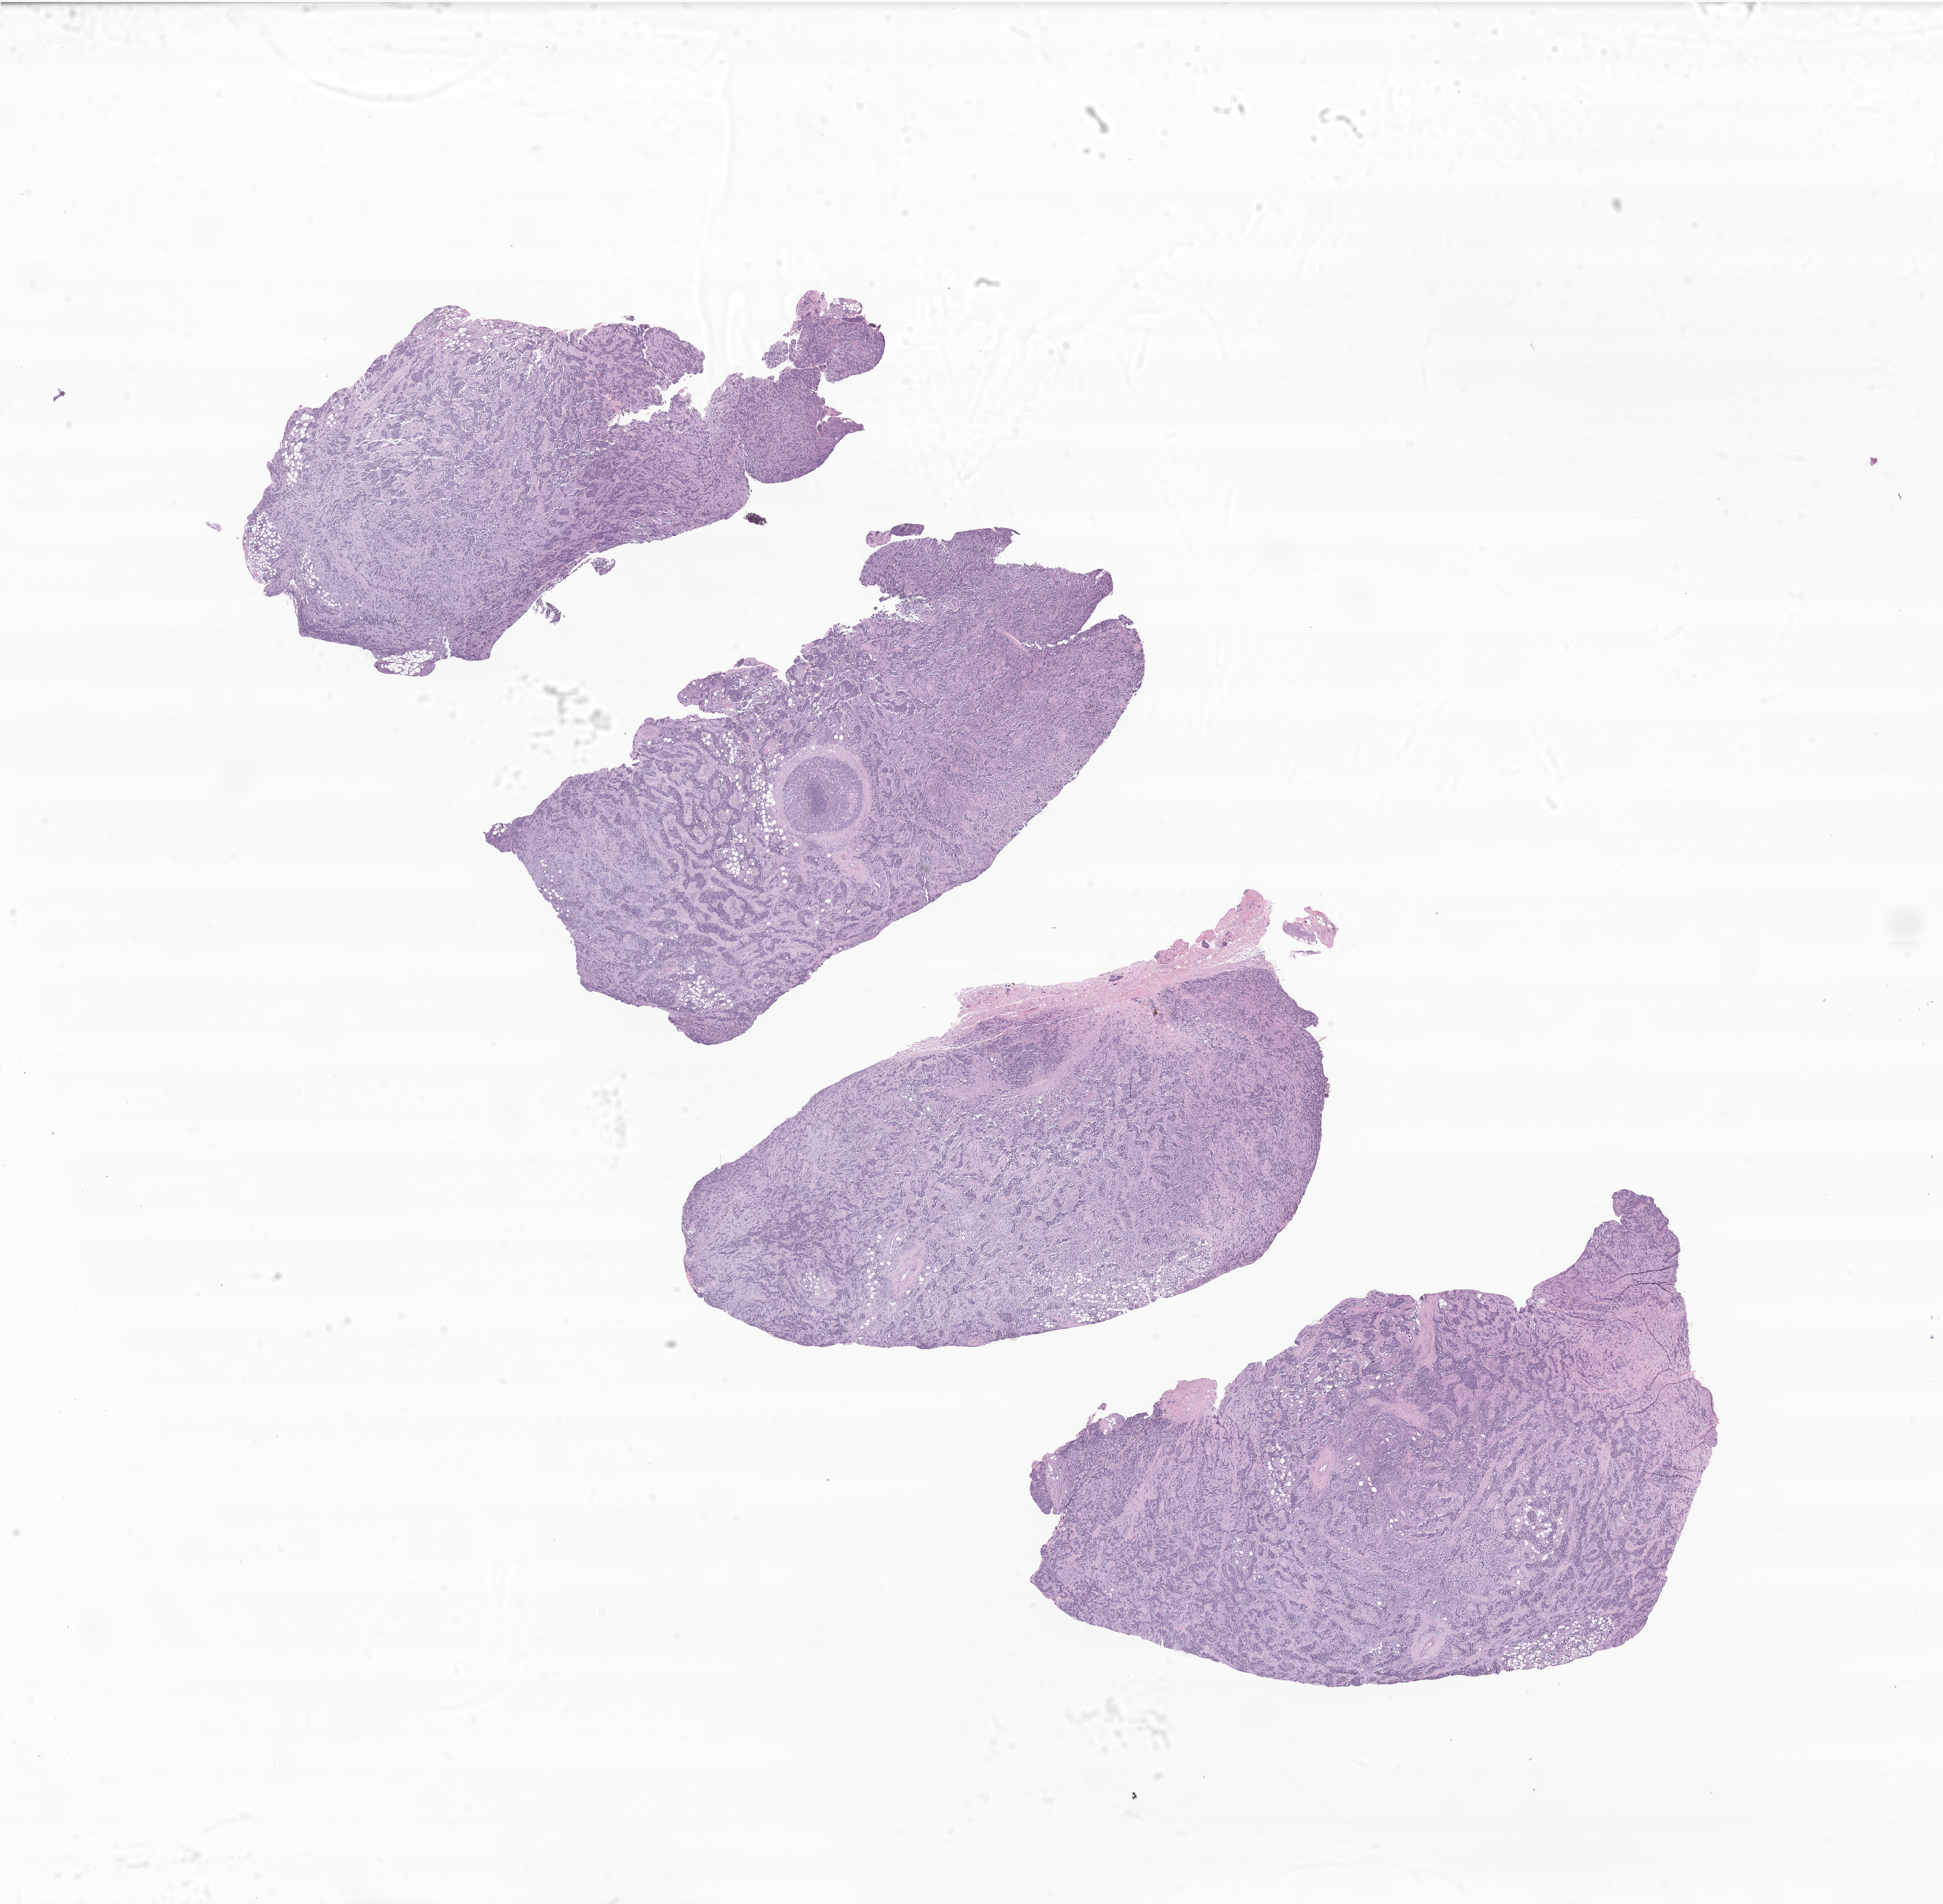
Digitized hematoxylin and eosin (H&E)-stained section of tumor tissue from the long bone of upper limb, whole scanned area (about 23.7 x 23.2 mm) shown as a low-resolution overview; formalin-fixed paraffin-embedded section. Male patient, age 125 months (10 years 5 months).
Recorded diagnosis: Rhabdomyosarcoma, NOS. Tissue or organ of origin (case record): long bones of upper limb, scapula and associated joints.